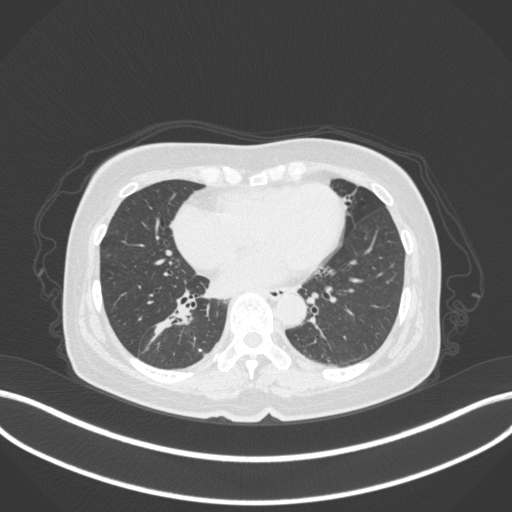
Chest CT, one axial slice; slice 159 of 429 in the series (ordered by position); reconstruction kernel B31f; 120 kVp; lung window (W 1500 / L -600 HU); 1 mm slice thickness; 512 × 512 image matrix, field of view 400 × 400 mm. Female patient, age 67 years. Case-level facts recorded for this patient, not image findings: clinical TNM (as recorded): T1c N1 M0.
Annotated regions visible in this slice (rectangle marked by the reading radiologist):
- lung tumour (recorded histology: adenocarcinoma): box from (x=144, y=301) to (x=192, y=340) px